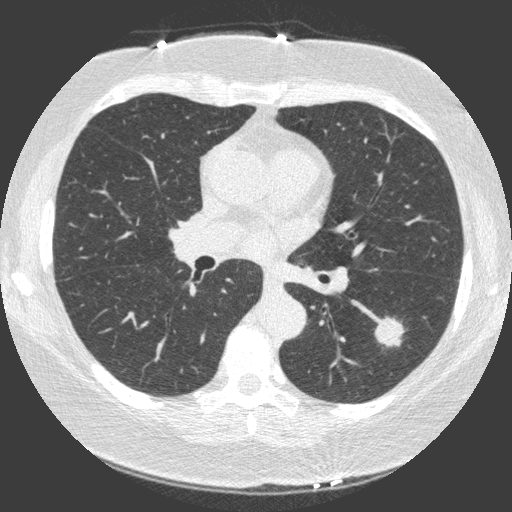
Low-dose screening chest CT, one axial slice; position 88 of 149 along the scan axis; lung window (W 1500 / L -600 HU); 1 mm slice thickness; 512 × 512 image matrix, field of view 330 × 330 mm.
Annotated regions visible in this slice (expert manual segmentation):
- lesion 1 (tumor, lower lobe of left lung): bounding box (x1, y1, x2, y2) in pixels: (375, 317, 405, 347)